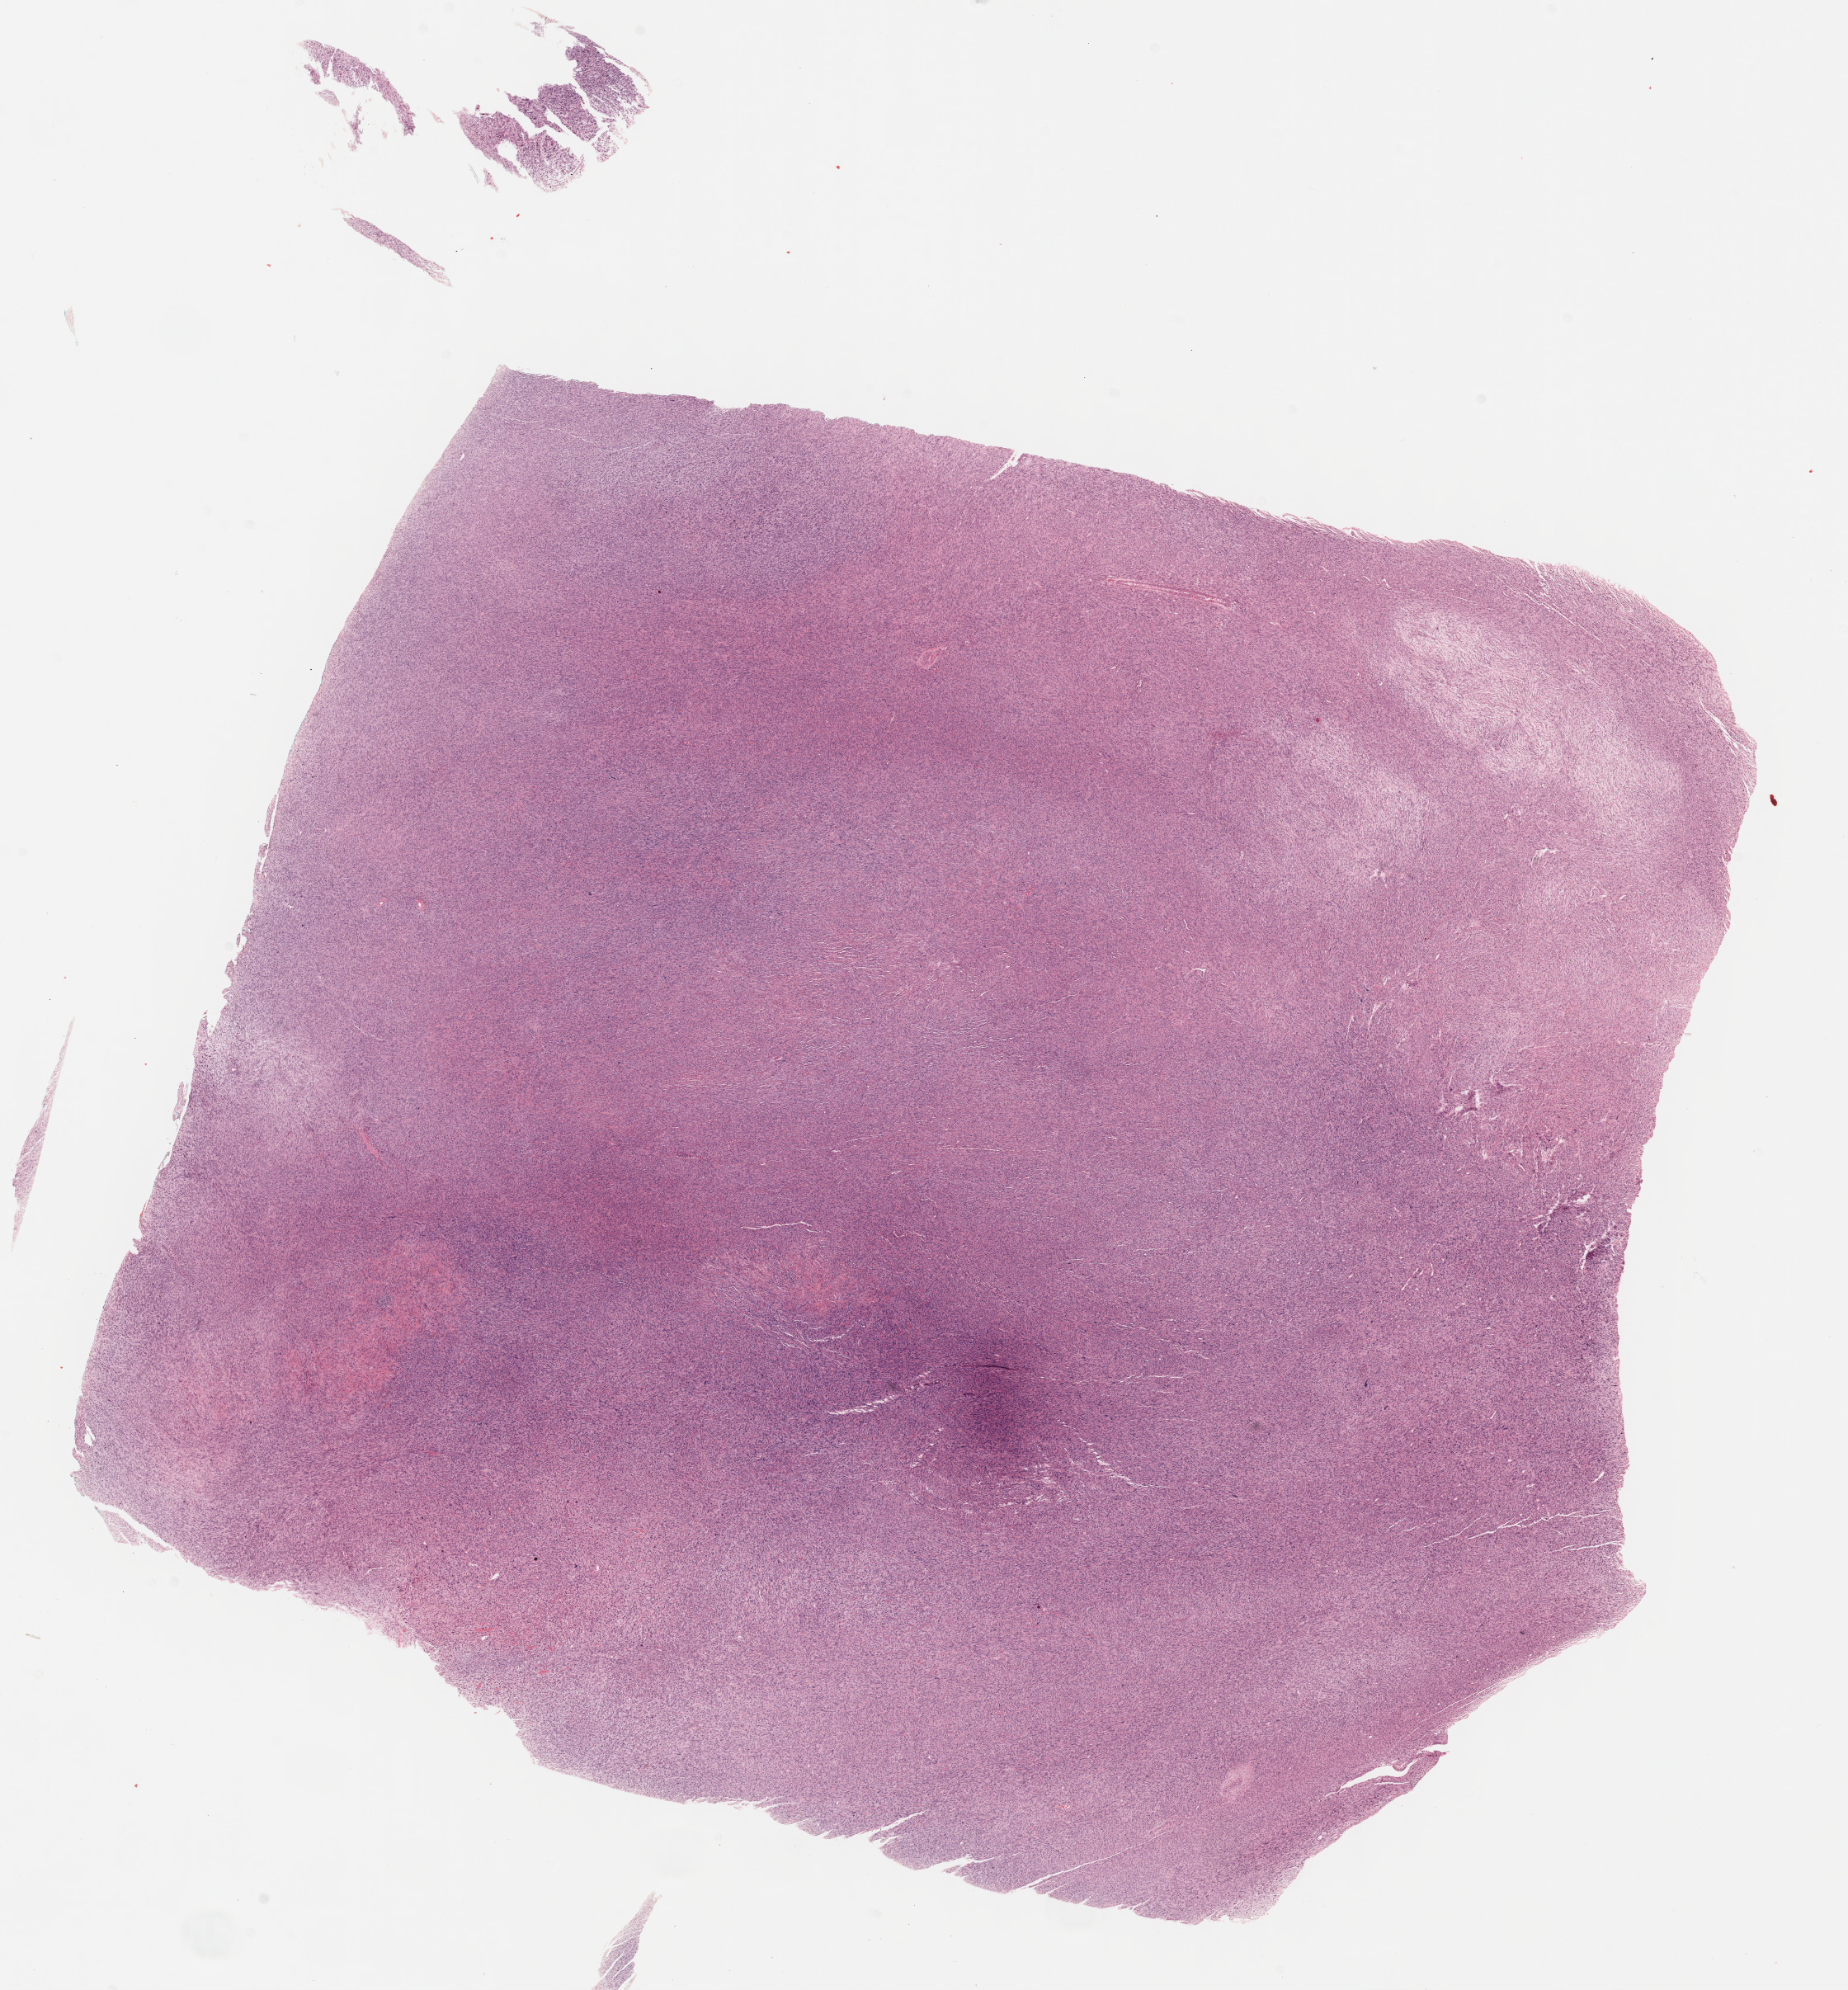
Digitized Hematoxylin and eosin (H&E) stained tissue section (whole slide), a low-resolution overview of the entire scanned area, about 18.1 x 19.5 mm (from a 40x scan); FFPE section; sample: primary tumour, retroperitoneum and peritoneum. Patient: male, age at initial diagnosis 61 years.
Pathologic diagnosis: Dedifferentiated liposarcoma (retroperitoneum).